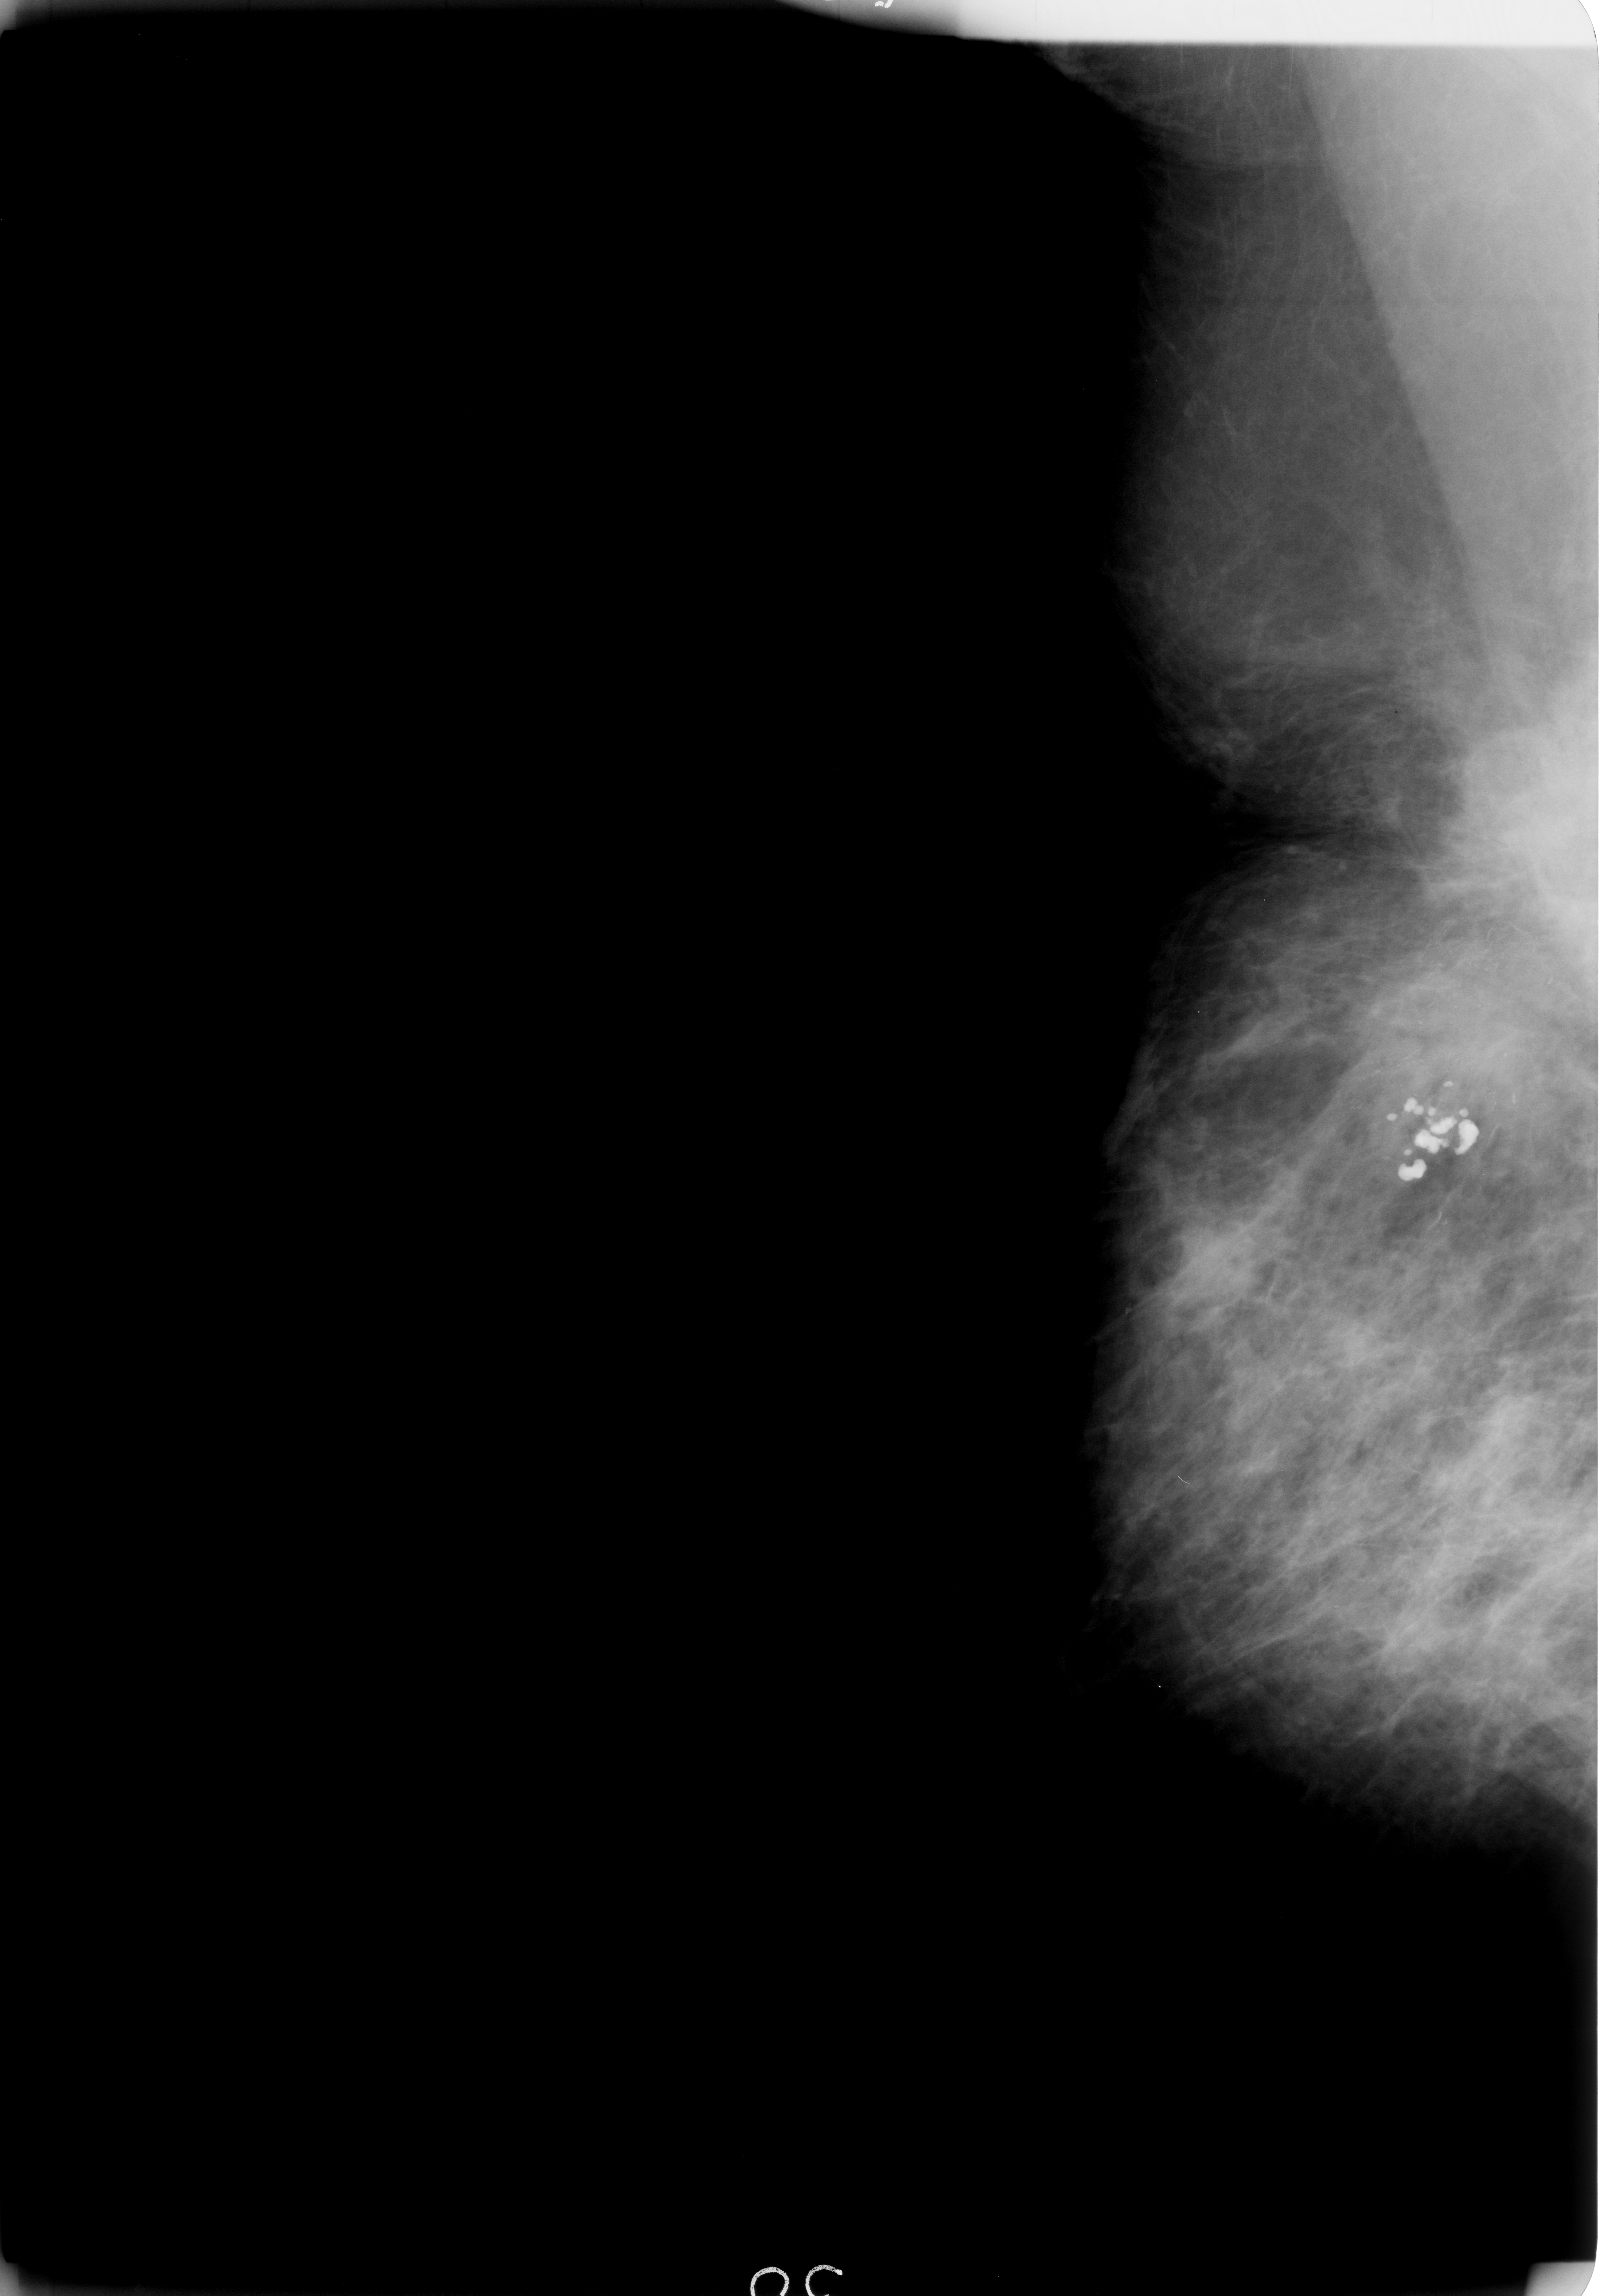
Digitized screen-film mammogram; right breast; mediolateral oblique (MLO) view; breast composition: scattered fibroglandular densities (BI-RADS density category 2 of 4).
- Radiologist-marked abnormalities on this image: Finding 1 of 3: calcifications, morphology pleomorphic / fine linear branching, distribution segmental; BI-RADS assessment category 5; subtlety rating 5 on a 1 (subtle) to 5 (obvious) scale; pathology result (as recorded, not read from the image): malignant.
- Finding 2 of 3: calcifications, morphology pleomorphic / fine linear branching, distribution segmental; BI-RADS assessment category 5; pathology (as recorded): malignant.
- Finding 3 of 3: calcifications, morphology pleomorphic / fine linear branching, distribution segmental; BI-RADS assessment category 5; pathology result (as recorded, not read from the image): malignant.